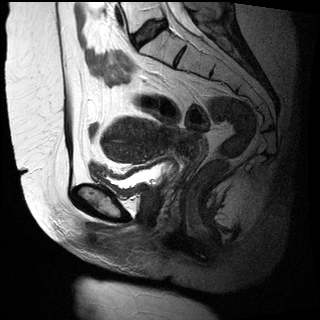
Pelvic MRI for cervical cancer, one sagittal slice. Slice 14 of 27 in the series (ordered by position). T2-weighted. 1.5 T. TE 89 ms, TR 2740 ms. 4 mm slice thickness. 320 × 320 image matrix. Patient: female, 47 years.
Structures marked on this image (manually delineated by an expert):
- uterus and cervix: box from (x=98, y=117) to (x=203, y=162) px